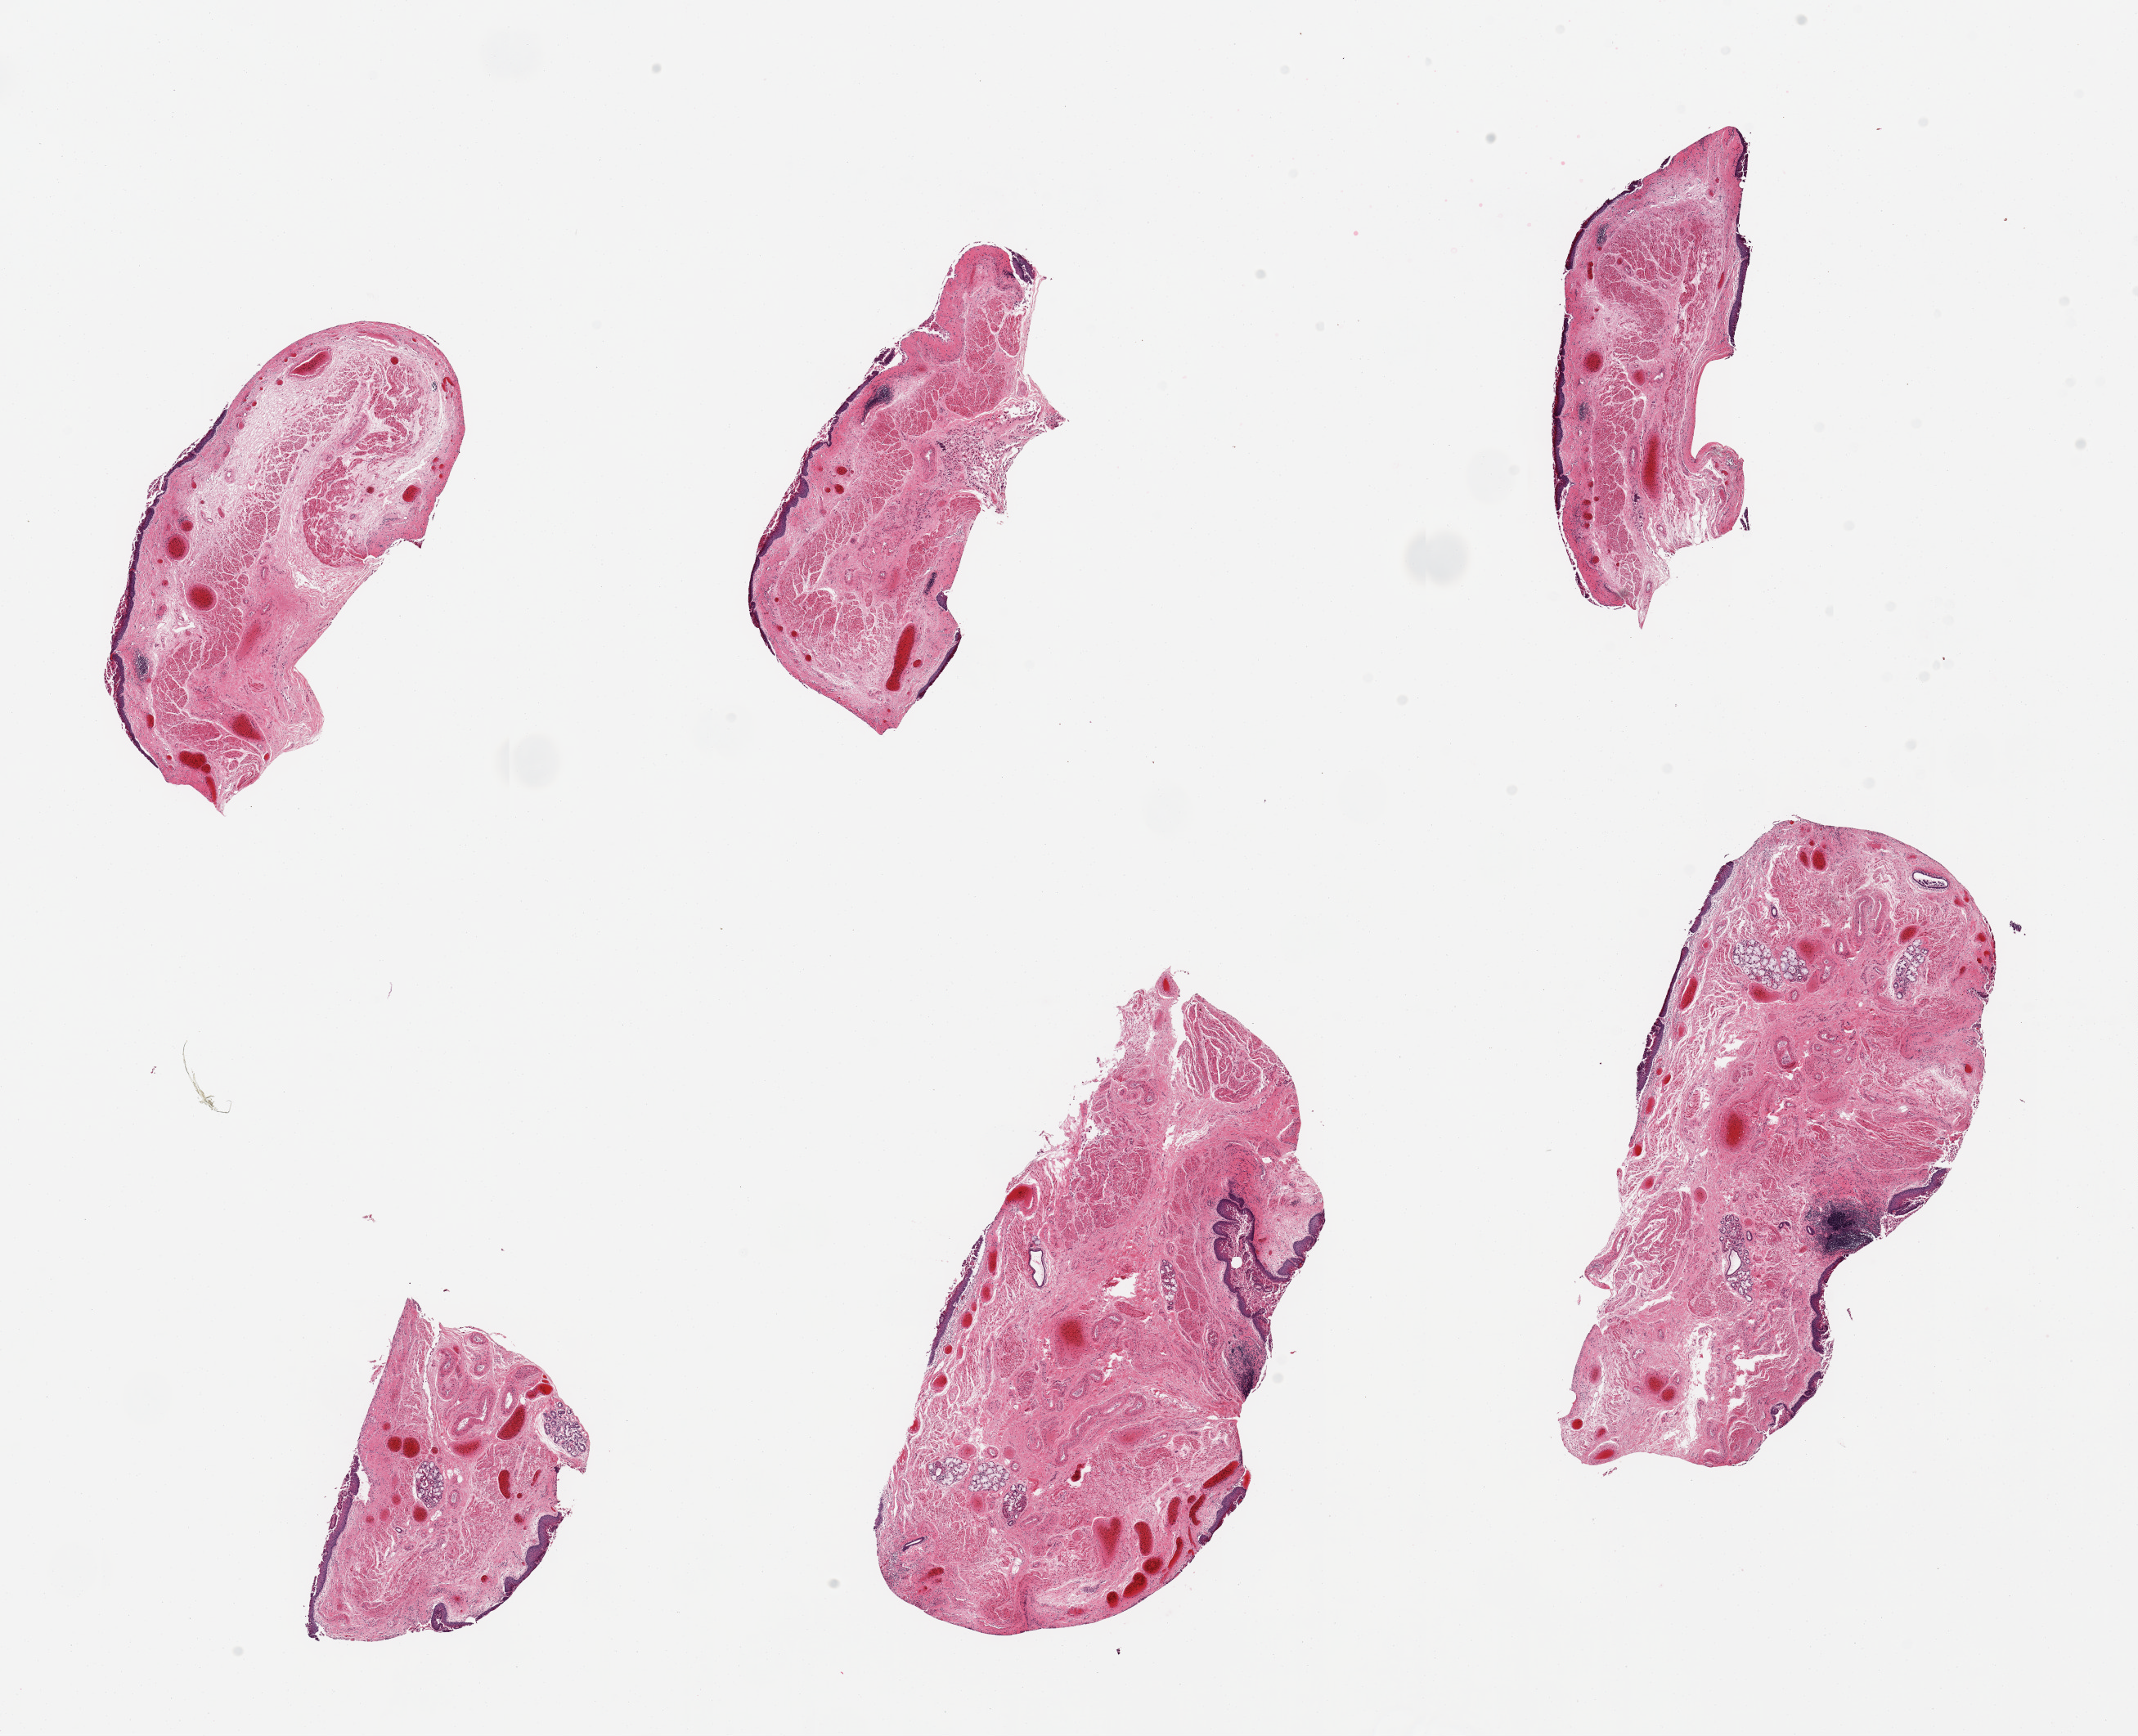
Whole-slide image, hematoxylin and eosin (H&E) stain, brightfield — shown as a low-resolution overview of the whole scanned area (about 20.7 x 16.8 mm, slide scanned at 20x). PAXgene-fixed, paraffin-embedded tissue. Target tissue: esophageal mucous membrane. Tissue donor sample. Donor sex: female.
Reviewer comment on this tissue sample: 6 pieces, squamous mucosa largely sloughed, few mucus glands; chronic esophagitis (ref foci).